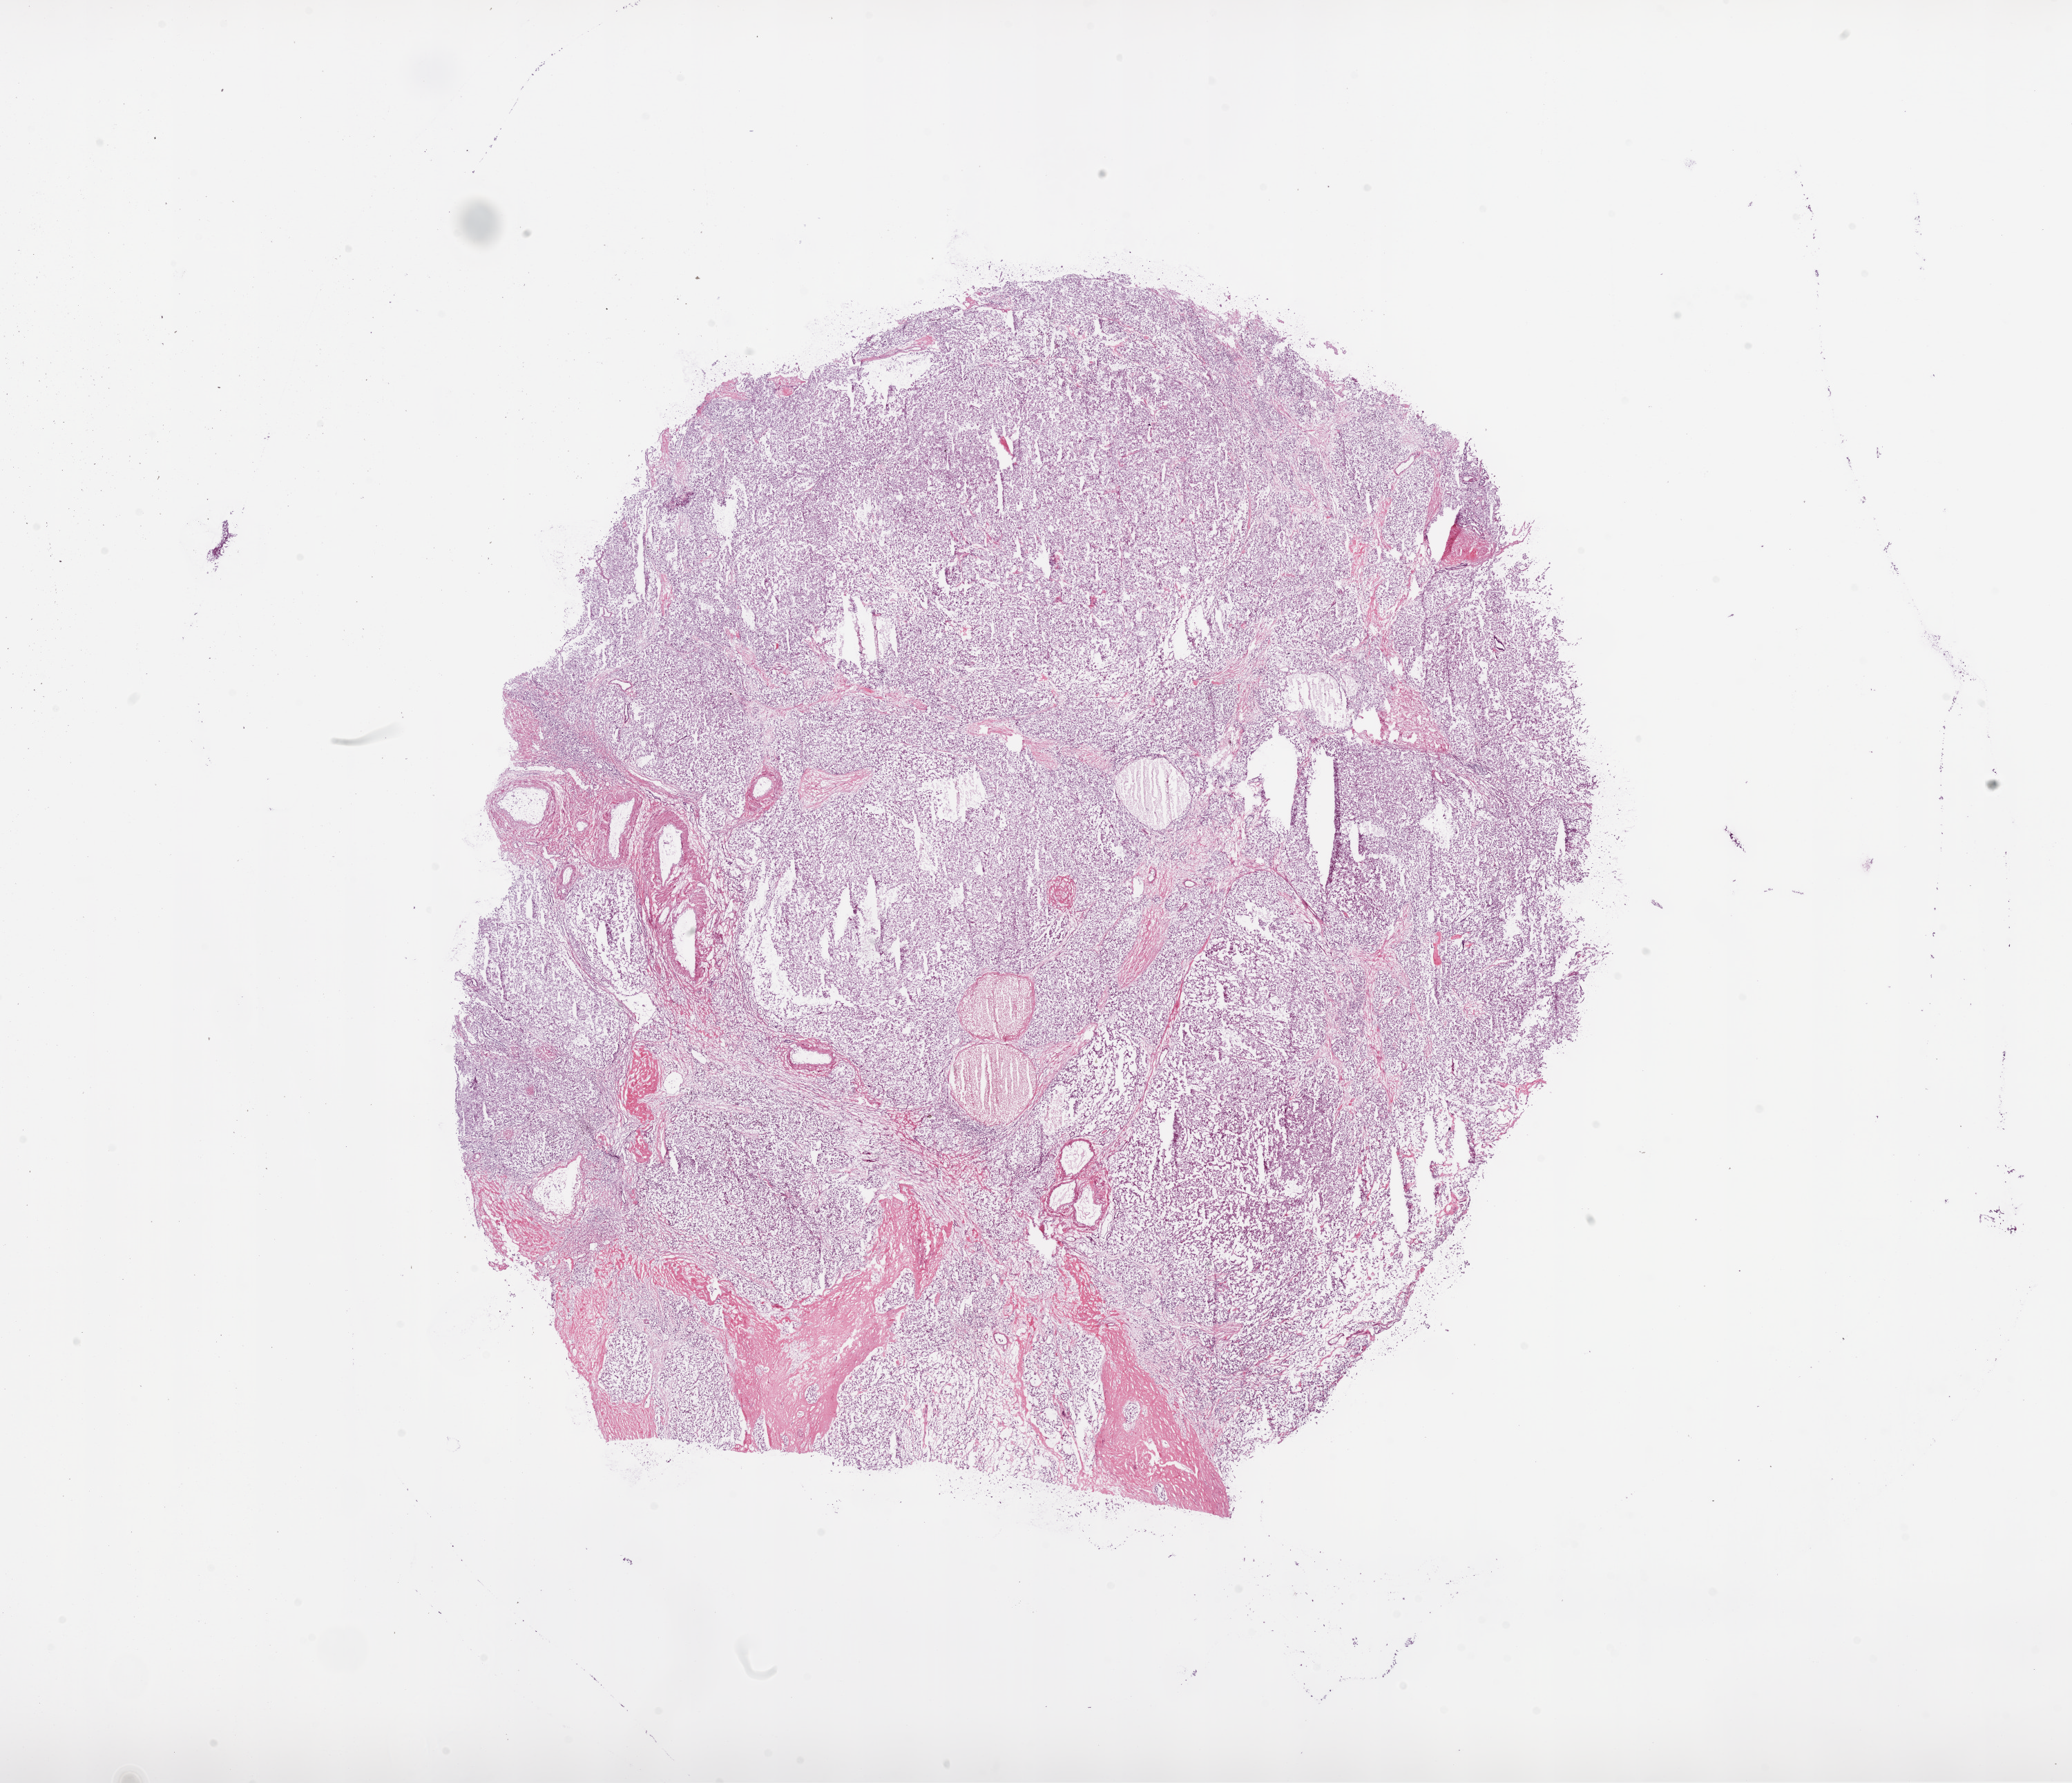
Whole-slide histology image, H&E, low-resolution overview of the scanned area, about 24.1 x 20.7 mm (from a 20x scan), frozen section, kidney, primary tumour sample. Patient: male, age at initial diagnosis 63 years. Histologic grade: G3 (poorly differentiated). Slide review estimates, as recorded: tumour cells 82%, tumour nuclei 80%, normal cells 0%, stromal cells 15%, necrosis 3%.
TNM: T1a N0 M0. Laterality: left. Pathologic diagnosis: Clear cell adenocarcinoma, NOS. AJCC pathologic stage: I.